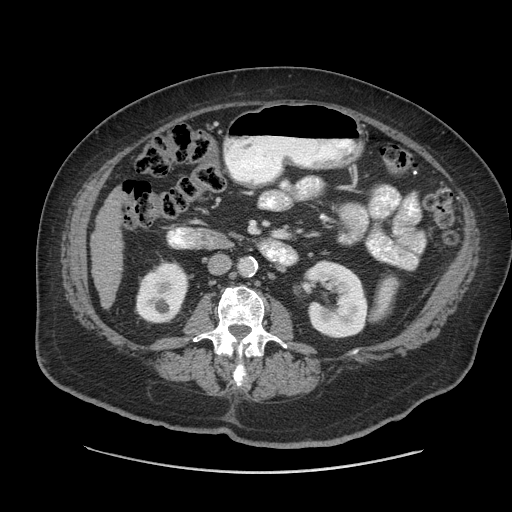
Contrast-enhanced abdominal CT (liver protocol), one axial slice. Position 15 of 91 along the scan axis. Reconstruction kernel STANDARD. Soft-tissue window (W 400 / L 40 HU). 2.5 mm slice thickness. 512 × 512 image matrix. From the clinical record (not read from this slice): diagnosis: hepatocellular carcinoma (patient treated with transarterial chemoembolisation; whether this scan precedes or follows treatment is not stated here); TNM stage (as recorded): Stage-I; Child-Pugh class: A; tumour differentiation: well differentiated.
Outlined on this slice (semi-automatic segmentation, software-assisted and operator-edited):
- liver parenchyma outside the tumour (the mass and vessels are separate outlines, so this box may not span the whole liver): bounding box [x1, y1, x2, y2] px = [90, 192, 124, 308]